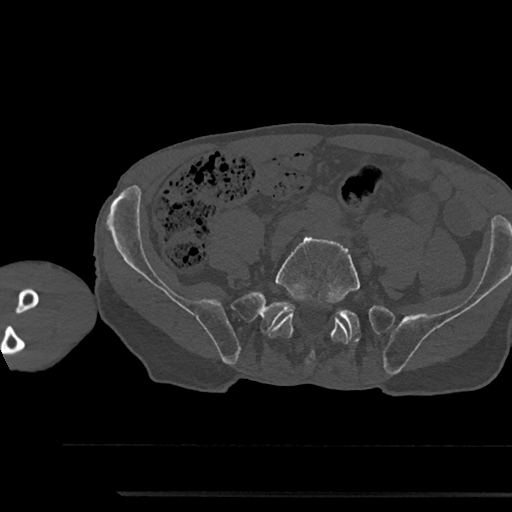
CT including the spine, one axial slice; slice 330 of 797 in the series (ordered by position); reconstruction kernel Br40s/3; bone window (W 1800 / L 400 HU); 0.5 mm slice thickness; 512 × 512 image matrix, field of view 367 × 367 mm. Patient: male, 79 years. Case-level facts recorded for this patient, not image findings: primary cancer: prostate.
Structures marked on this image (semi-automatic segmentation, software-assisted and operator-edited):
- L5 vertebra: bounding box <267,237,360,364> (left, top, right, bottom; pixels)